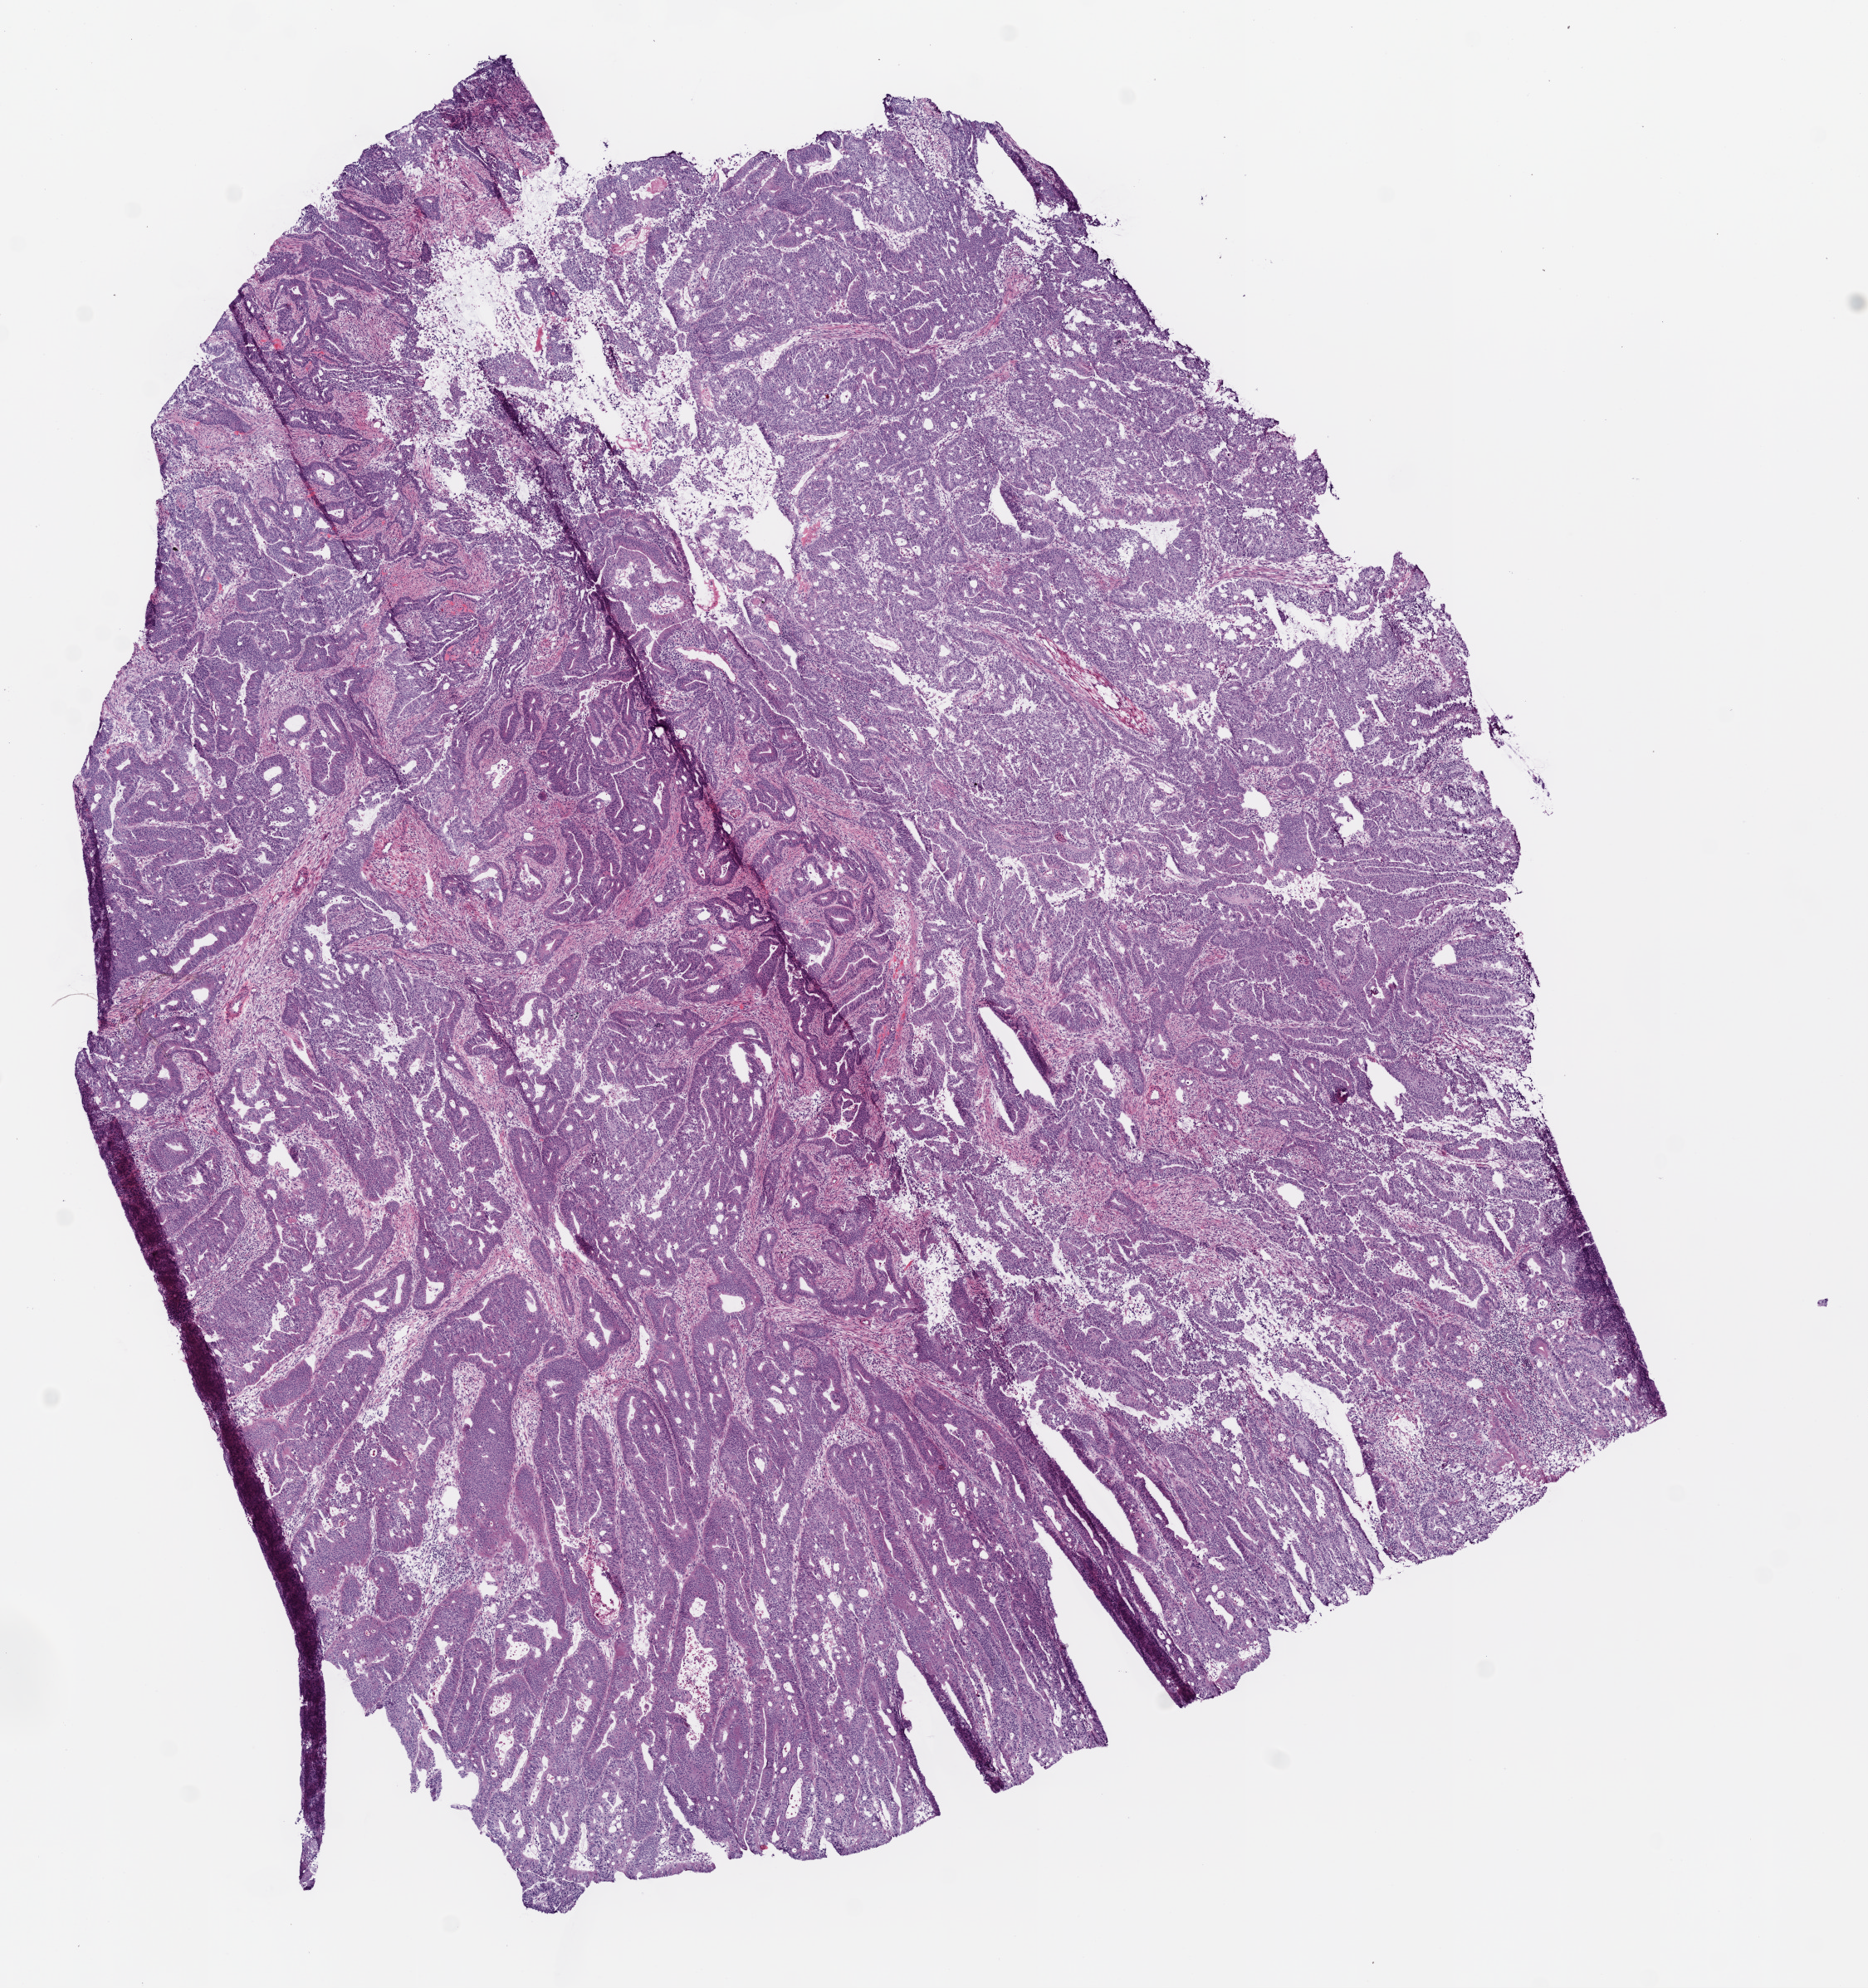
Whole-slide histology image, Hematoxylin and eosin (H&E) stained, a low-resolution overview of the entire scanned area, about 9.0 x 9.6 mm, frozen section from the top of the tissue portion, primary tumour sample from the colon. Female patient; age at initial diagnosis 71 years. Slide review estimates, as recorded: tumour cells 85%, tumour nuclei 90%, normal cells 0%, stromal cells 14%, necrosis 1%.
* AJCC pathologic stage: IIIC (6th edition)
* TNM: T3 N2 M0
* pathologic diagnosis: Adenocarcinoma, NOS